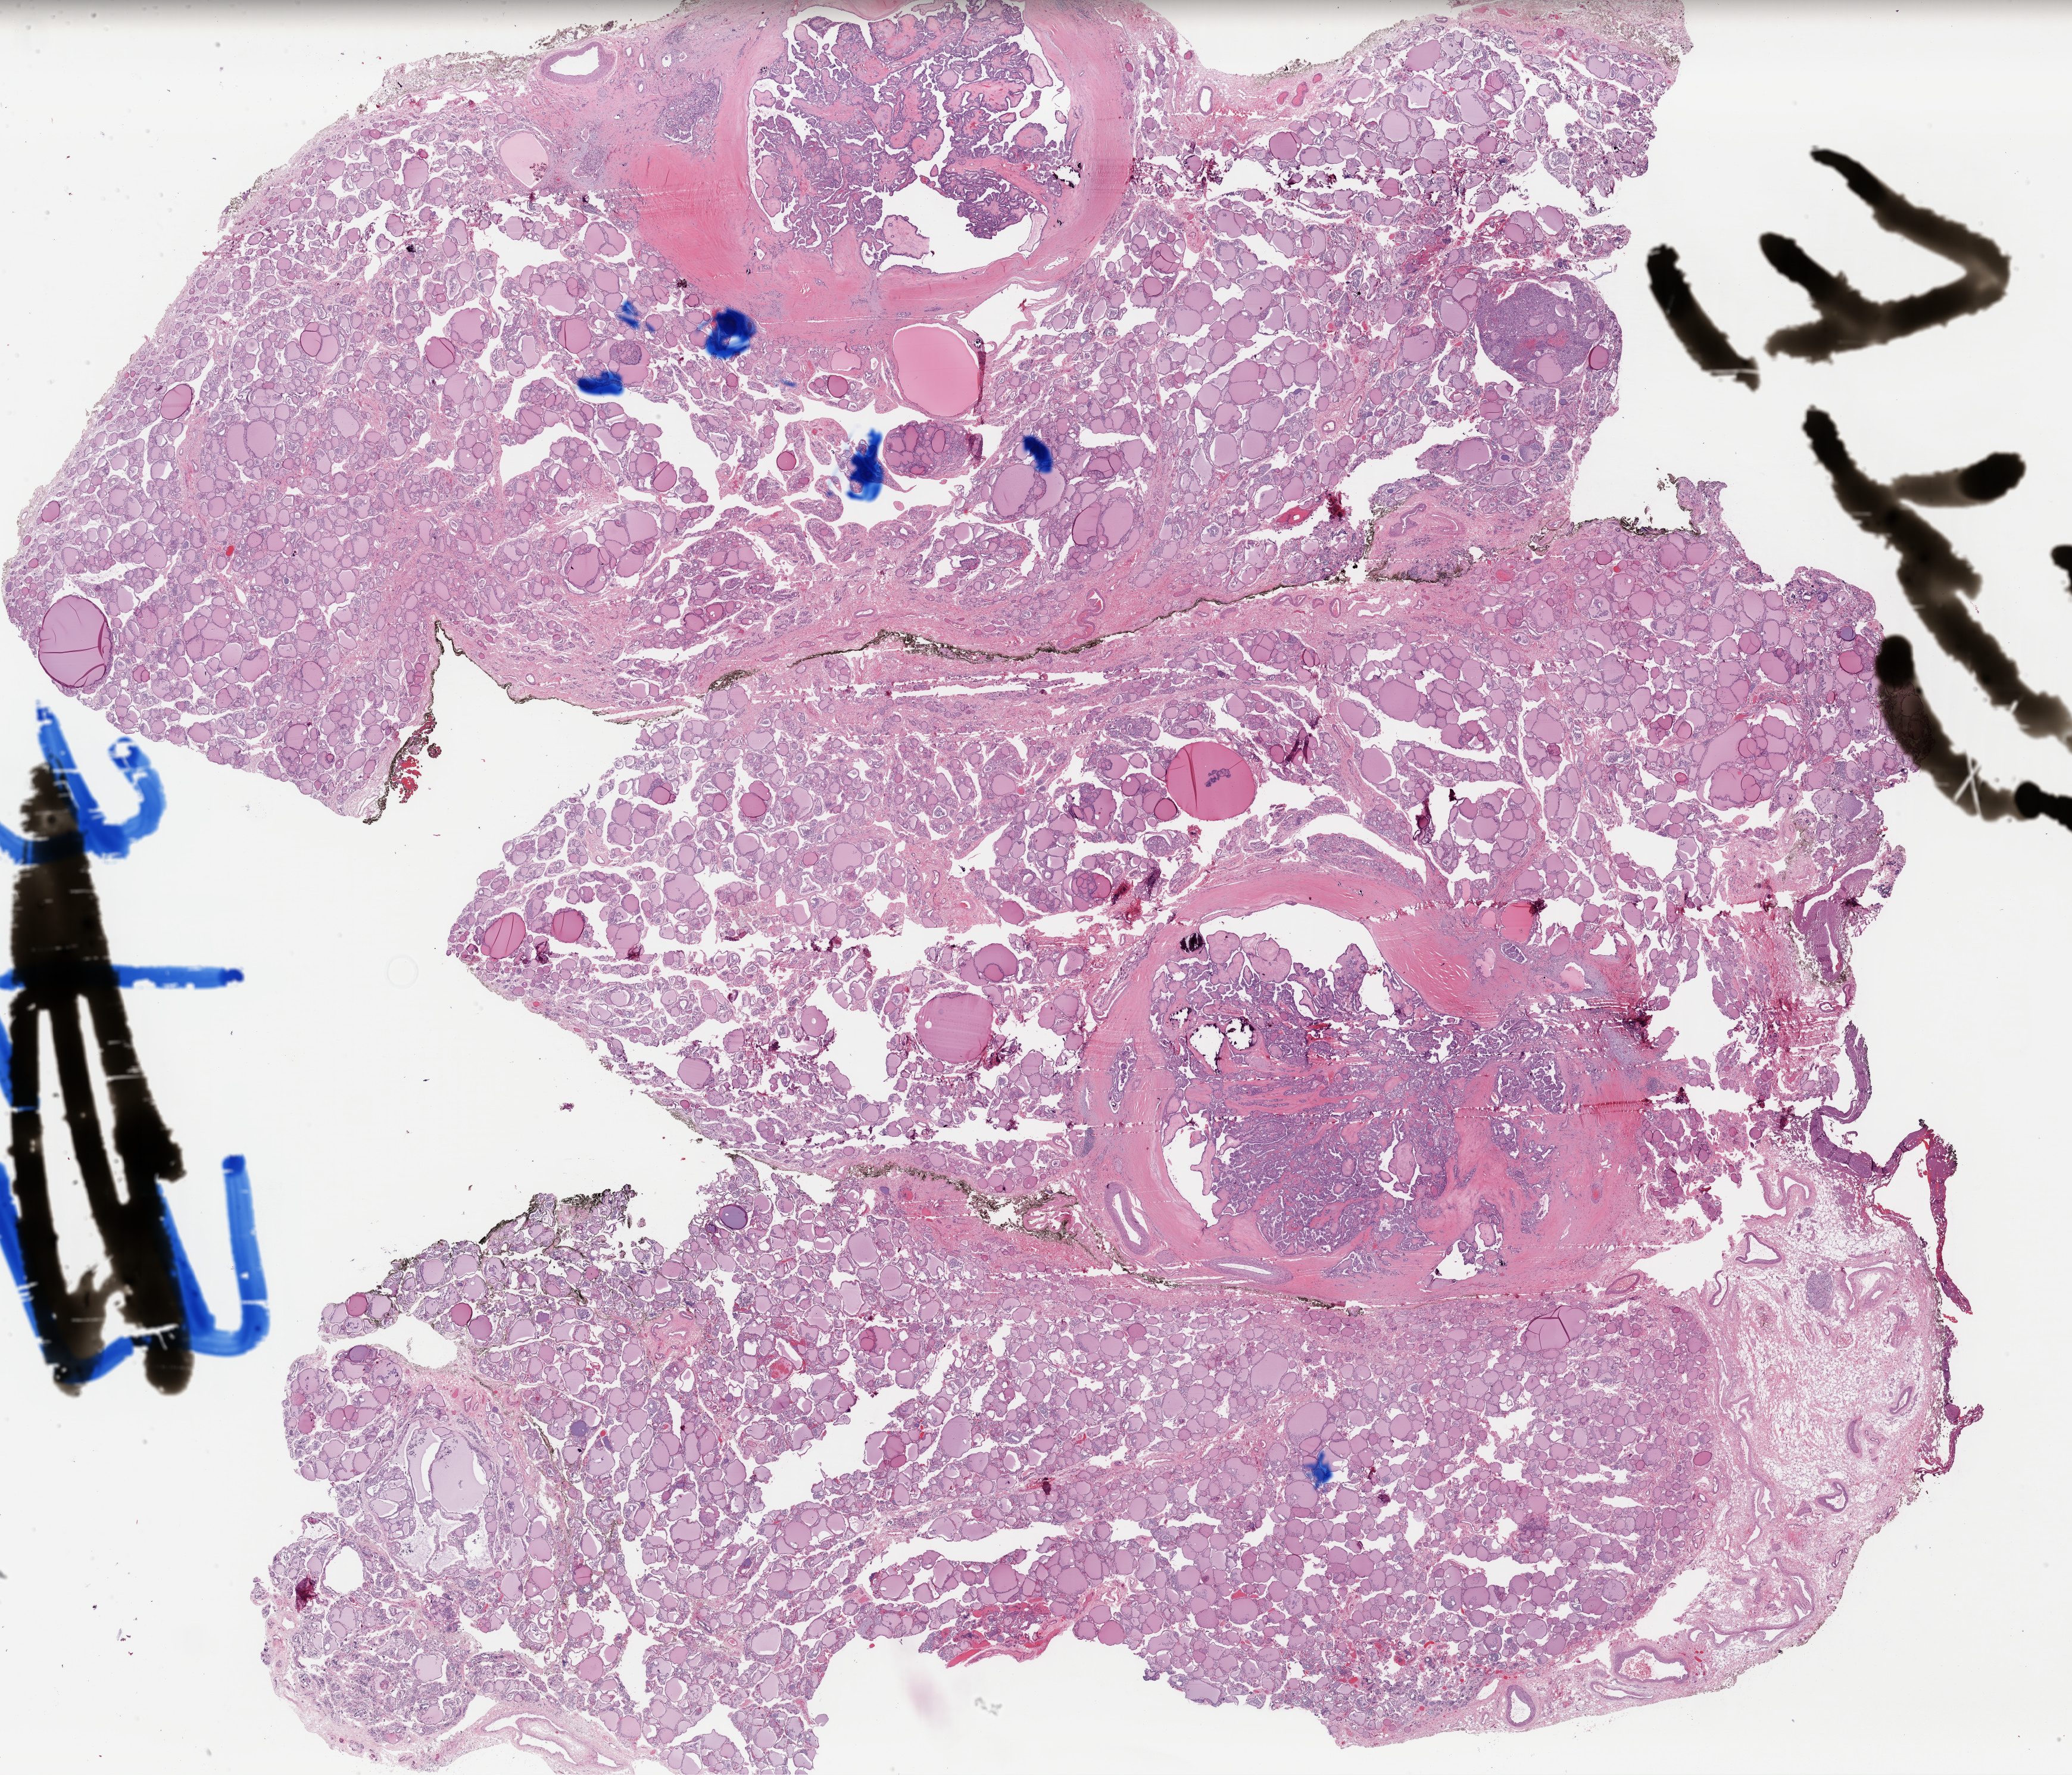
Whole-slide histology image, Hematoxylin and eosin (H&E) stained — whole scanned area (about 27.5 x 23.5 mm, from a 40x scan) shown as a low-resolution overview; formalin-fixed paraffin-embedded (FFPE) diagnostic section; primary tumour sample from the thyroid. Male patient; age at initial diagnosis 78 years.
• laterality: left
• AJCC pathologic stage: III
• lymph nodes positive (case pathology): 0 of 2 examined
• pathologic diagnosis: Papillary adenocarcinoma, NOS (thyroid gland)